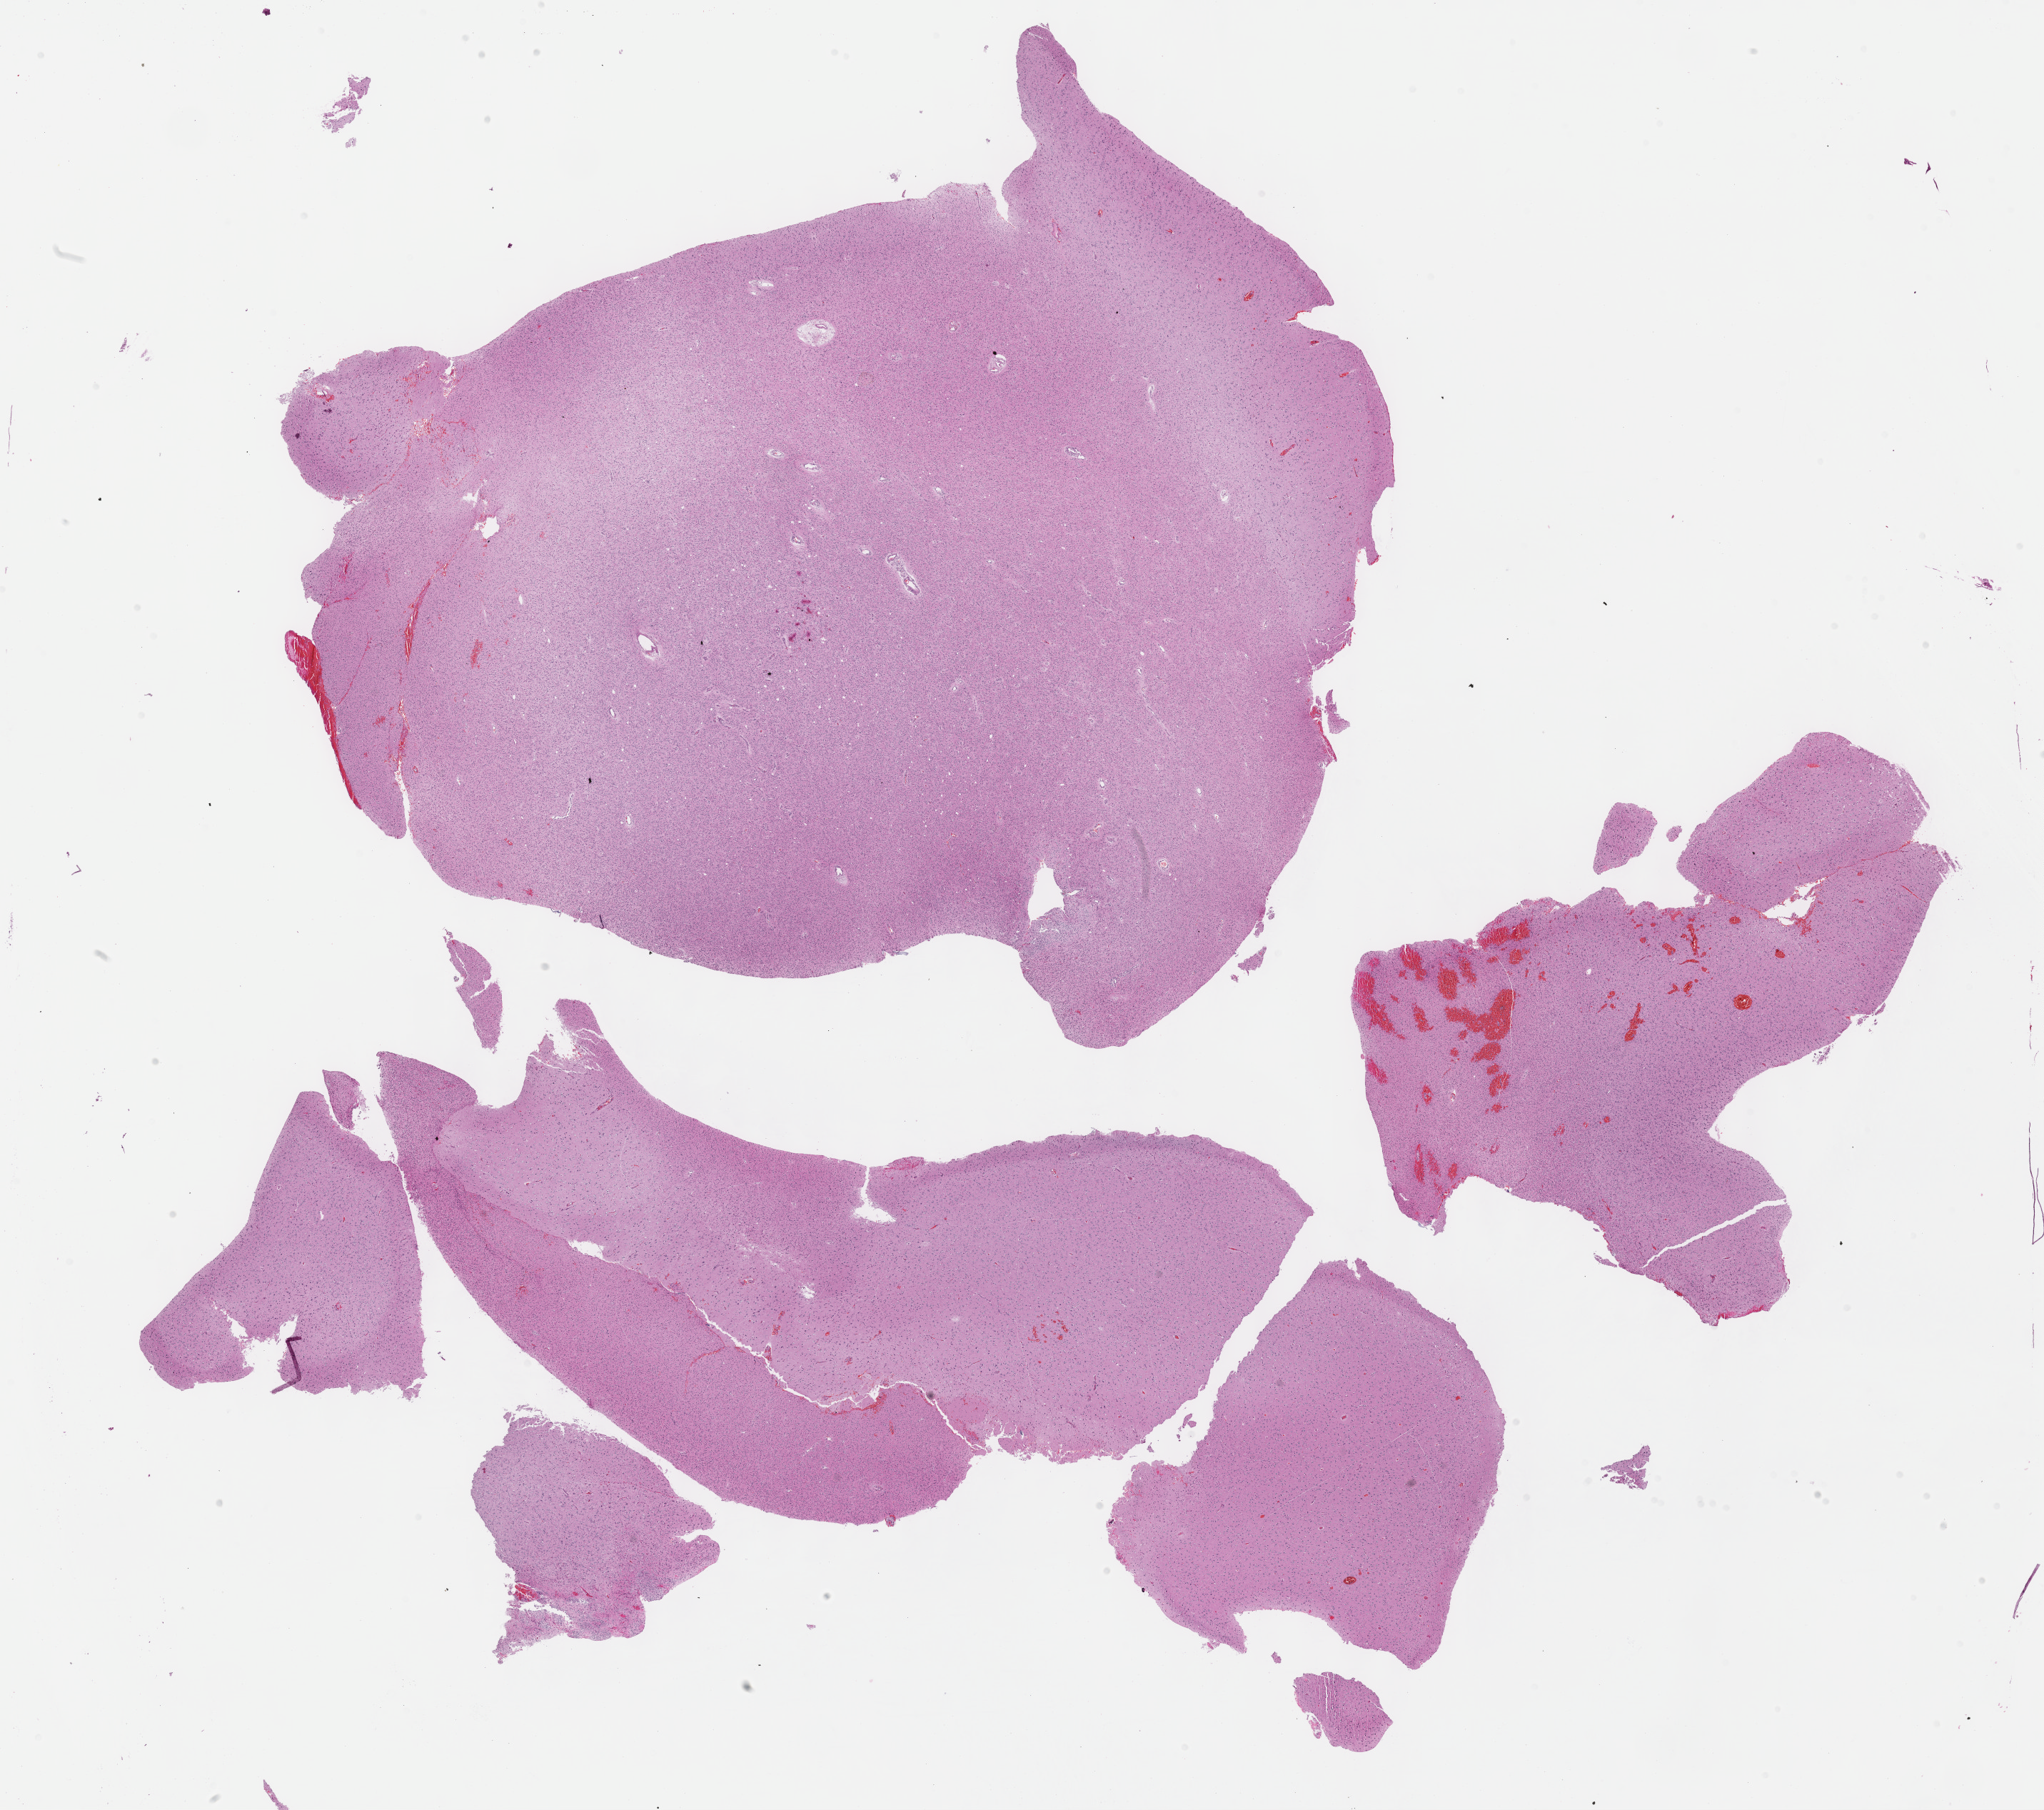
Digitized Hematoxylin and eosin (H&E) stained tissue section (whole slide) — a low-resolution overview of the entire scanned area, about 23.2 x 20.5 mm (slide scanned at 40x), formalin-fixed paraffin-embedded (FFPE) diagnostic section, brain, primary tumour sample. Male, age 47 years at initial diagnosis. Histologic grade: G2 (moderately differentiated).
- histologic diagnosis: Oligodendroglioma, NOS (cerebrum)